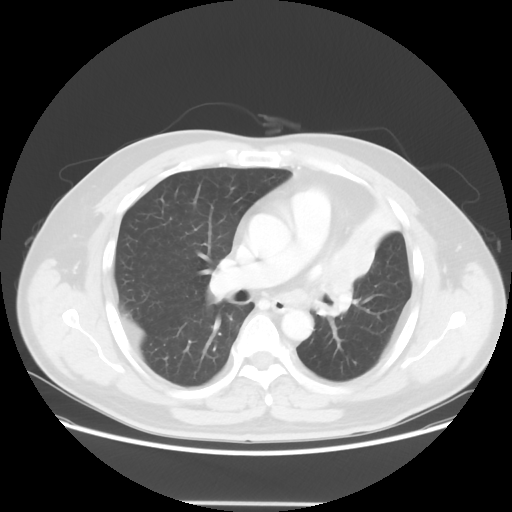
Chest CT, one axial slice. Slice 36 of 62 in the series (ordered by position). Reconstruction kernel STANDARD. Lung window (W 1500 / L -600 HU). 5 mm slice thickness. 512 × 512 image matrix. Male patient, age 49 years. From the clinical record (not read from this slice): clinical TNM (as recorded): T3 N3 M1c.
Structures marked on this image (rectangle marked by the reading radiologist):
- lung tumour (recorded histology: squamous cell carcinoma): box from (x=319, y=237) to (x=382, y=329) px